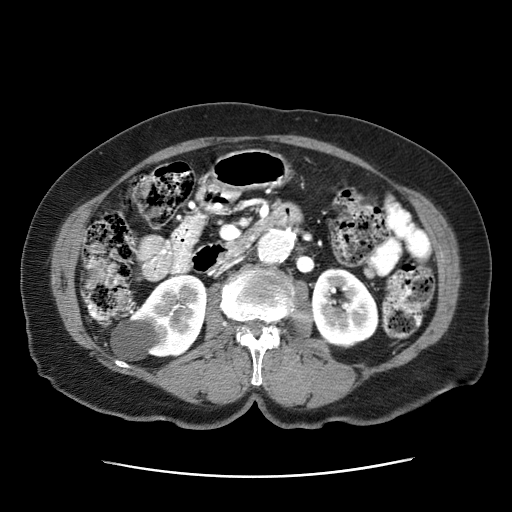
Contrast-enhanced abdominal CT (liver protocol), one axial slice; position 4 of 63 along the scan axis; reconstruction kernel STANDARD; 120 kVp; intravenous contrast given; soft-tissue window (W 400 / L 40 HU); 512 × 512 image matrix, field of view 360 × 360 mm. Female patient, age 79 years. From the clinical record (not read from this slice): diagnosis: hepatocellular carcinoma (patient treated with transarterial chemoembolisation; whether this scan precedes or follows treatment is not stated here); TNM stage (as recorded): Stage-II; Child-Pugh class: B; tumour differentiation: well differentiated; tumour nodularity: multinodular.
Outlined on this slice (semi-automatic segmentation, software-assisted and operator-edited):
- abdominal aorta: bounding box <257,228,294,263> (left, top, right, bottom; pixels)